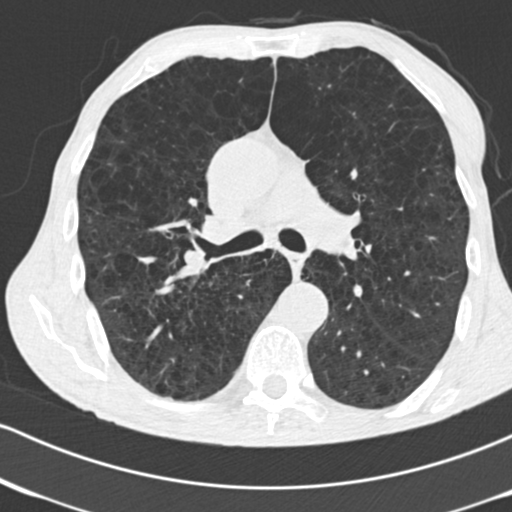
Low-dose screening chest CT, one axial slice. Position 105 of 182 along the scan axis. Reconstruction kernel B30f. 120 kVp. Lung window (W 1500 / L -600 HU). 2 mm slice thickness. 512 × 512 image matrix, field of view 316 × 316 mm.
Annotated regions visible in this slice (manually delineated by an expert):
- lesion 1 (tumor, lower lobe of right lung): box from (x=176, y=266) to (x=201, y=280) px